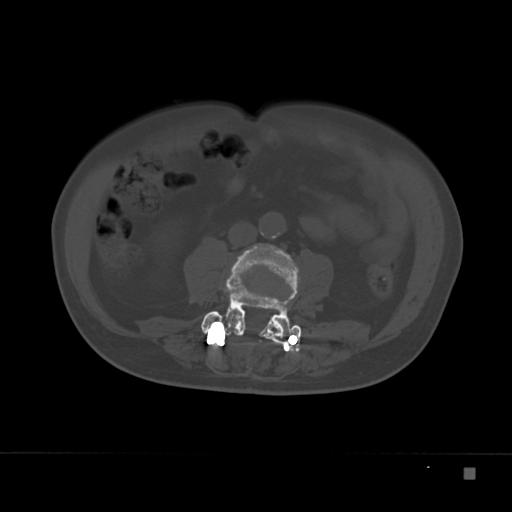
CT including the spine, one axial slice. Position 55 of 332 along the scan axis. Reconstruction kernel Br40s. 120 kVp. Bone window (W 1800 / L 400 HU). 1.5 mm slice thickness. 512 × 512 image matrix. Patient: male, 72 years. Case-level facts recorded for this patient, not image findings: primary cancer: skeletal.
Annotated regions visible in this slice (semi-automatic segmentation, software-assisted and operator-edited):
- L3 vertebra: bounding box [x1, y1, x2, y2] px = [226, 244, 300, 329]
- L4 vertebra: [201, 279, 302, 347]